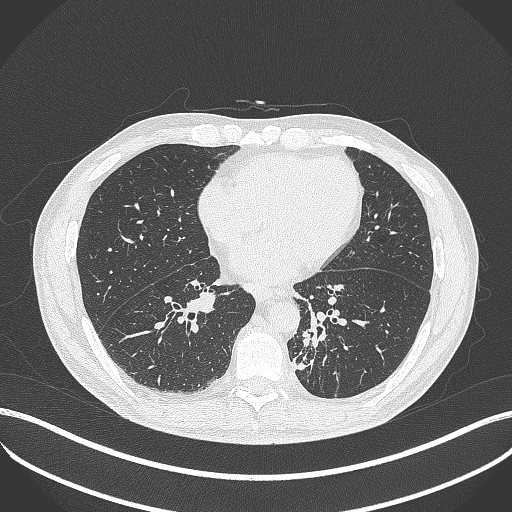
Chest CT, one axial slice; position 157 of 451 along the scan axis; reconstruction kernel B70f; 120 kVp; lung window (W 1500 / L -600 HU); 1 mm slice thickness; 512 × 512 image matrix. Male patient, age 72 years. Case-level facts recorded for this patient, not image findings: clinical TNM (as recorded): T2b N0 M1.
Outlined on this slice (bounding box drawn by a radiologist):
- lung tumour (recorded histology: adenocarcinoma): bounding box (x1, y1, x2, y2) in pixels: (292, 330, 319, 371)